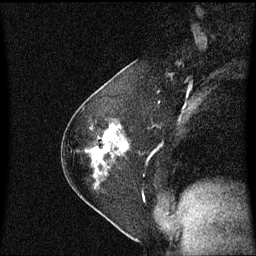
Breast MRI (dynamic contrast-enhanced), one sagittal slice; position 36 of 60 along the scan axis; dynamic contrast-enhanced series, image 2 of 3 at this slice position (ordered by acquisition); 1.5 T; TE 4.2 ms, TR 8.4 ms; 2 mm slice thickness; 256 × 256 image matrix, field of view 210 × 210 mm. Female patient, age 54 years. Case-level facts recorded for this patient, not image findings: setting: breast cancer imaged before/during neoadjuvant chemotherapy; receptor status: HER2-positive.
Annotated regions visible in this slice (semi-automatic segmentation, software-assisted and operator-edited):
- analysis volume of interest (the breast-tissue region the enhancement analysis was run in; not a lesion): bounding box [x1, y1, x2, y2] px = [87, 125, 130, 189]
- tumour enhancement mask (voxels above the 70 % enhancement threshold inside the analysis volume of interest): [104, 131, 129, 151]